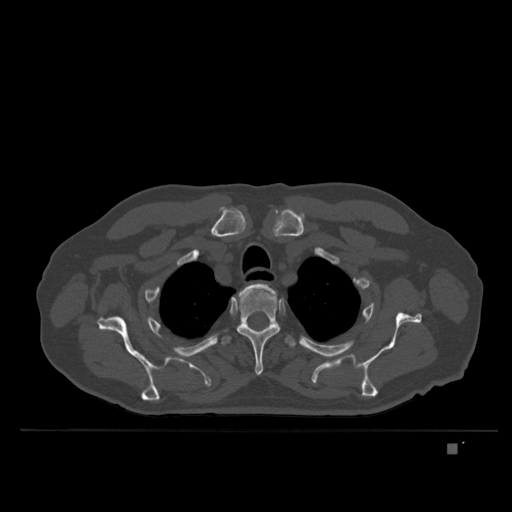
CT including the spine, one axial slice; position 300 of 435 along the scan axis; bone window (W 1800 / L 400 HU); 512 × 512 image matrix. Patient: male, 73 years. Case-level facts recorded for this patient, not image findings: primary cancer: skin.
Outlined on this slice (semi-automatic segmentation, software-assisted and operator-edited):
- T2 vertebra: bounding box (x1, y1, x2, y2) in pixels: (235, 283, 276, 301)
- T3 vertebra: (237, 284, 280, 376)
- T4 vertebra: (221, 335, 301, 348)